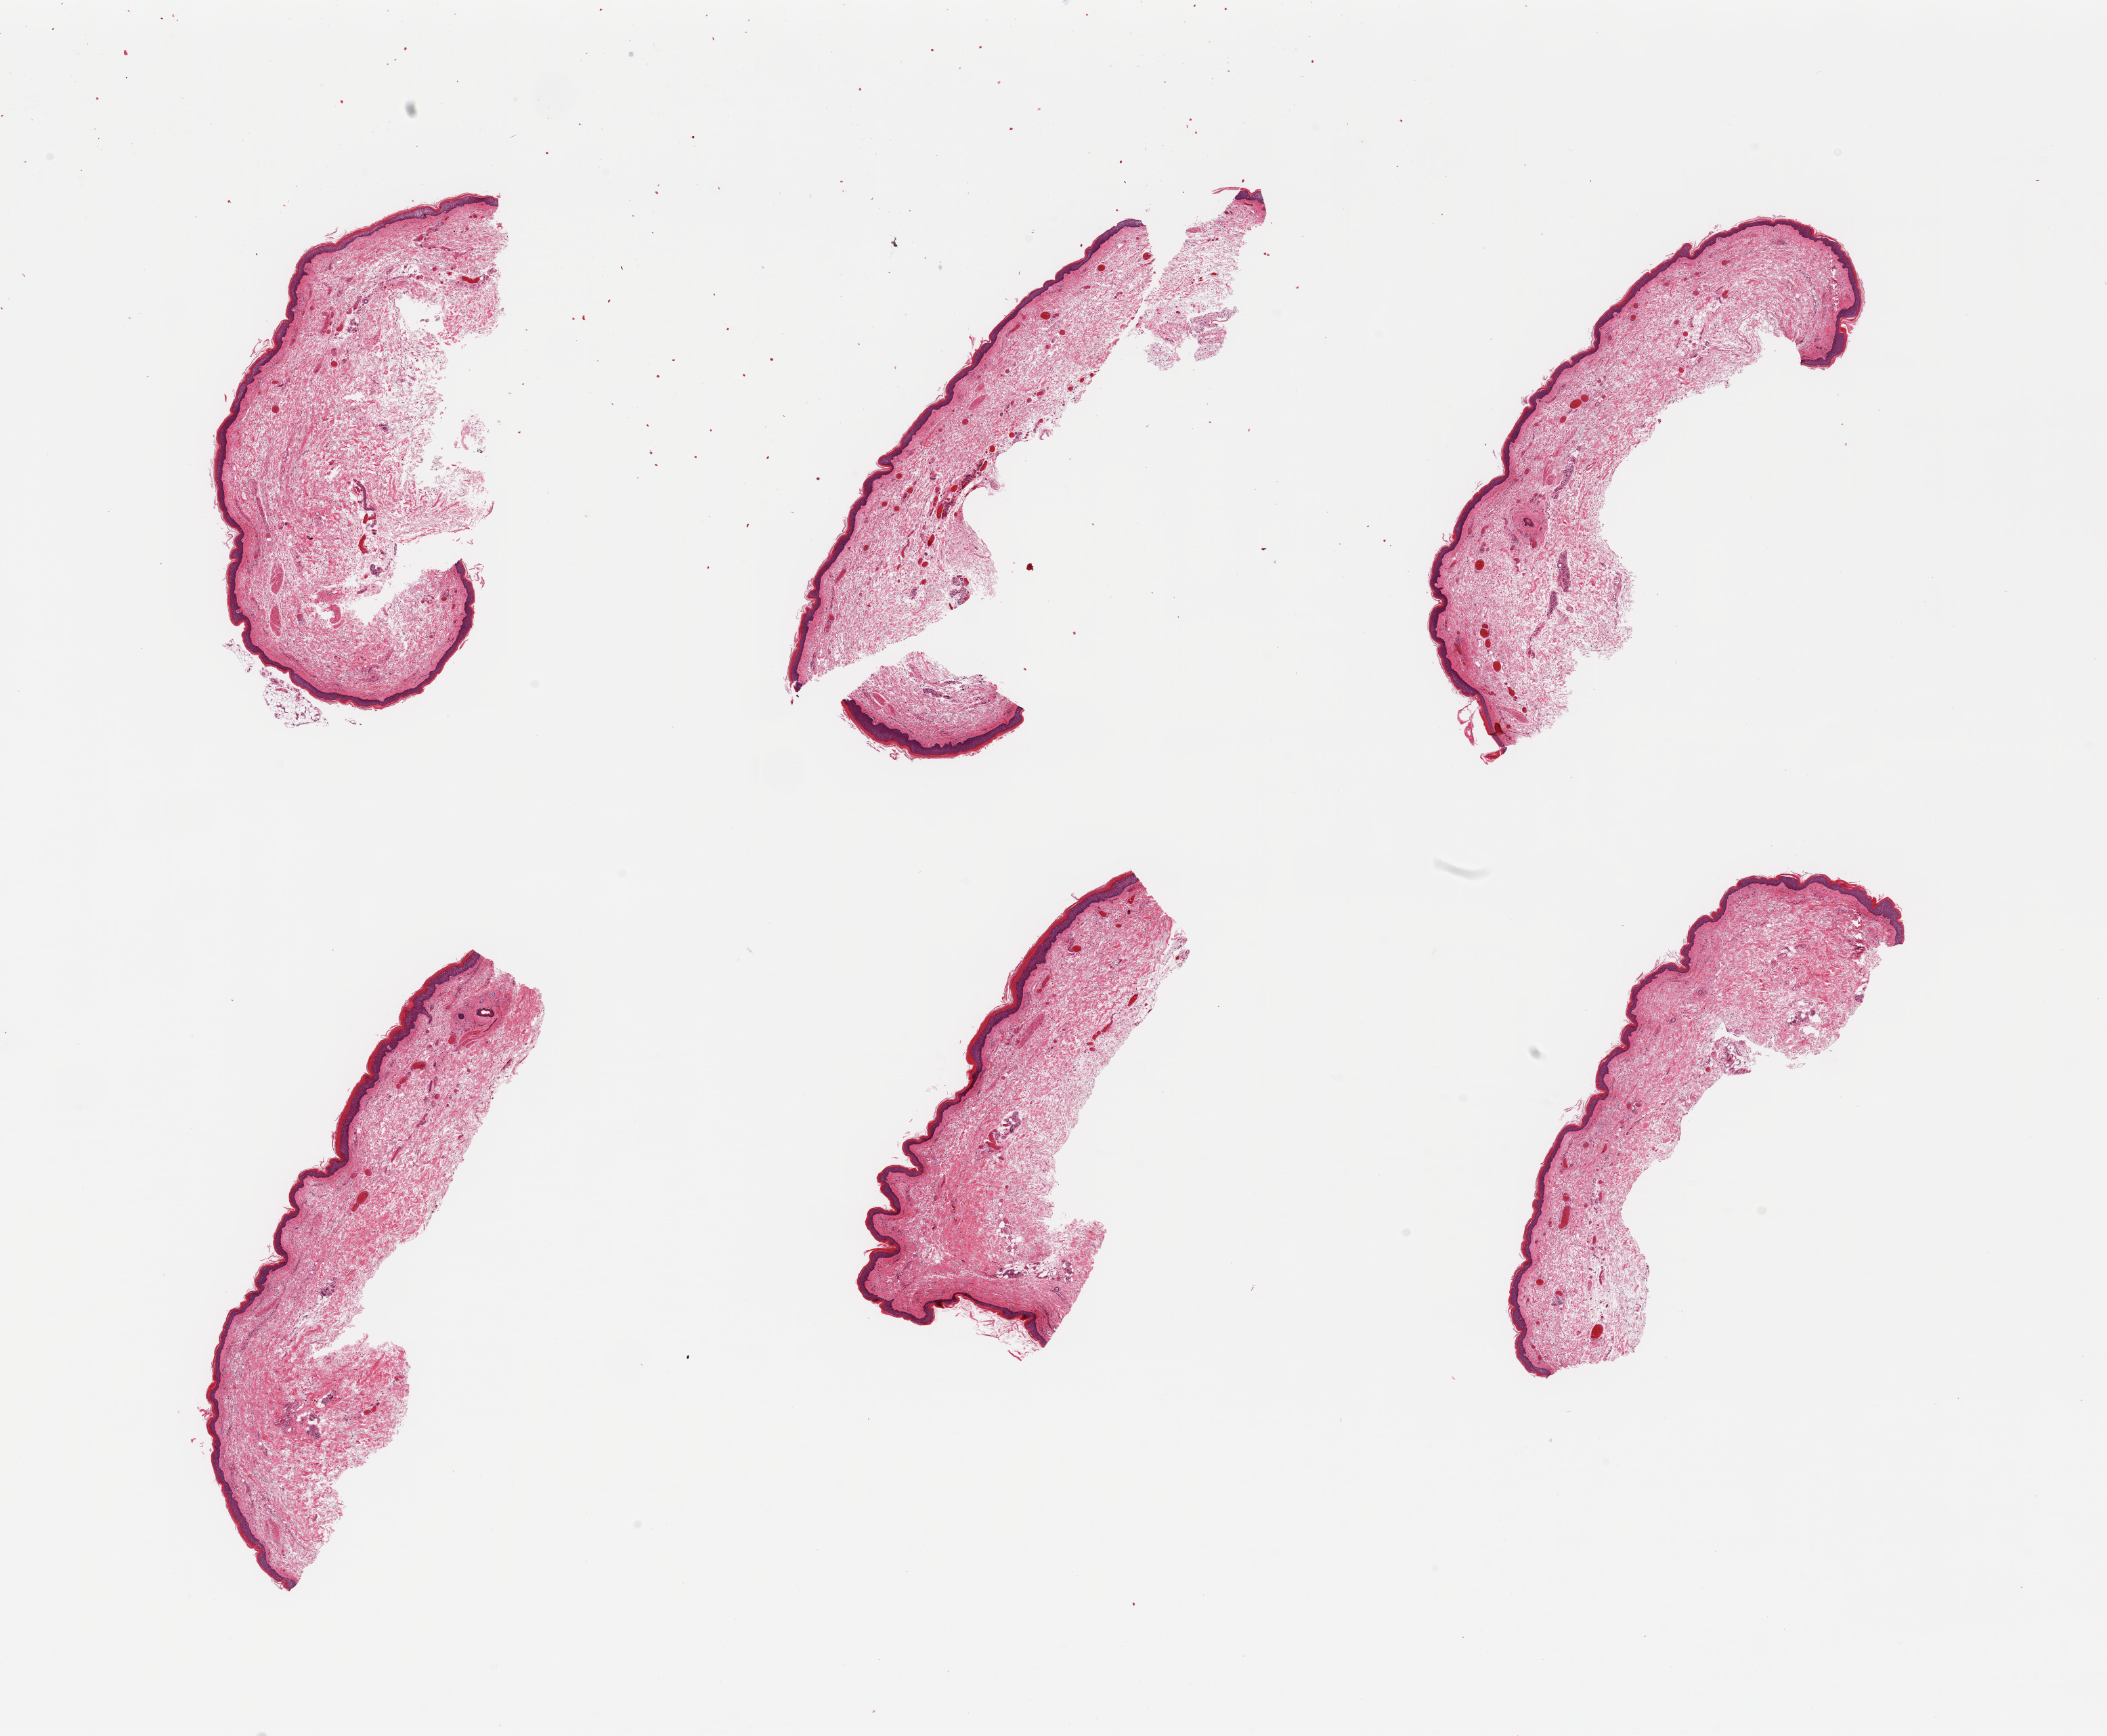
H&E whole-slide image, whole scanned area (about 24.6 x 20.3 mm, slide scanned at 20x) shown as a low-resolution overview. PAXgene-fixed, paraffin-embedded tissue. Sampled site (target tissue): skin of lower leg. Donor tissue sample. Female donor.
* pathologist's review note for this sample: 6 pieces, squamous epithelium up to ~ 60-70 microns. Minimal dermal fat